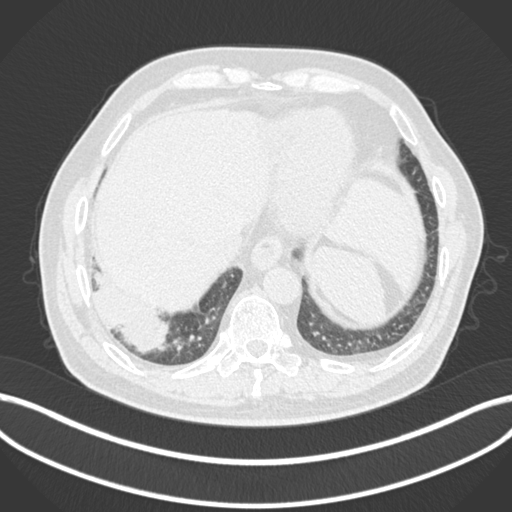
Chest CT, one axial slice; slice 23 of 200 in the series (ordered by position); lung window (W 1500 / L -600 HU); 512 × 512 image matrix, field of view 400 × 400 mm. Male patient, age 59 years.
Annotated regions visible in this slice (bounding box drawn by a radiologist):
- lung tumour (recorded histology: adenocarcinoma): bounding box (x1, y1, x2, y2) in pixels: (89, 269, 173, 356)